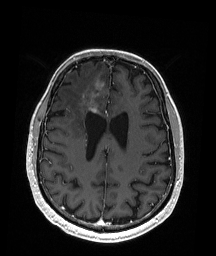
Brain MRI from a brain-tumour surgery series, one axial slice; slice 71 of 192 in the series (ordered by position); T1-weighted post-contrast; 216 × 256 image matrix, field of view 211 × 250 mm. From the clinical record (not read from this slice): histopathology: Astrocytoma; WHO grade: 3; IDH mutation: yes.
Outlined on this slice (expert manual segmentation):
- tumour: bounding box [x1, y1, x2, y2] px = [84, 94, 98, 114]